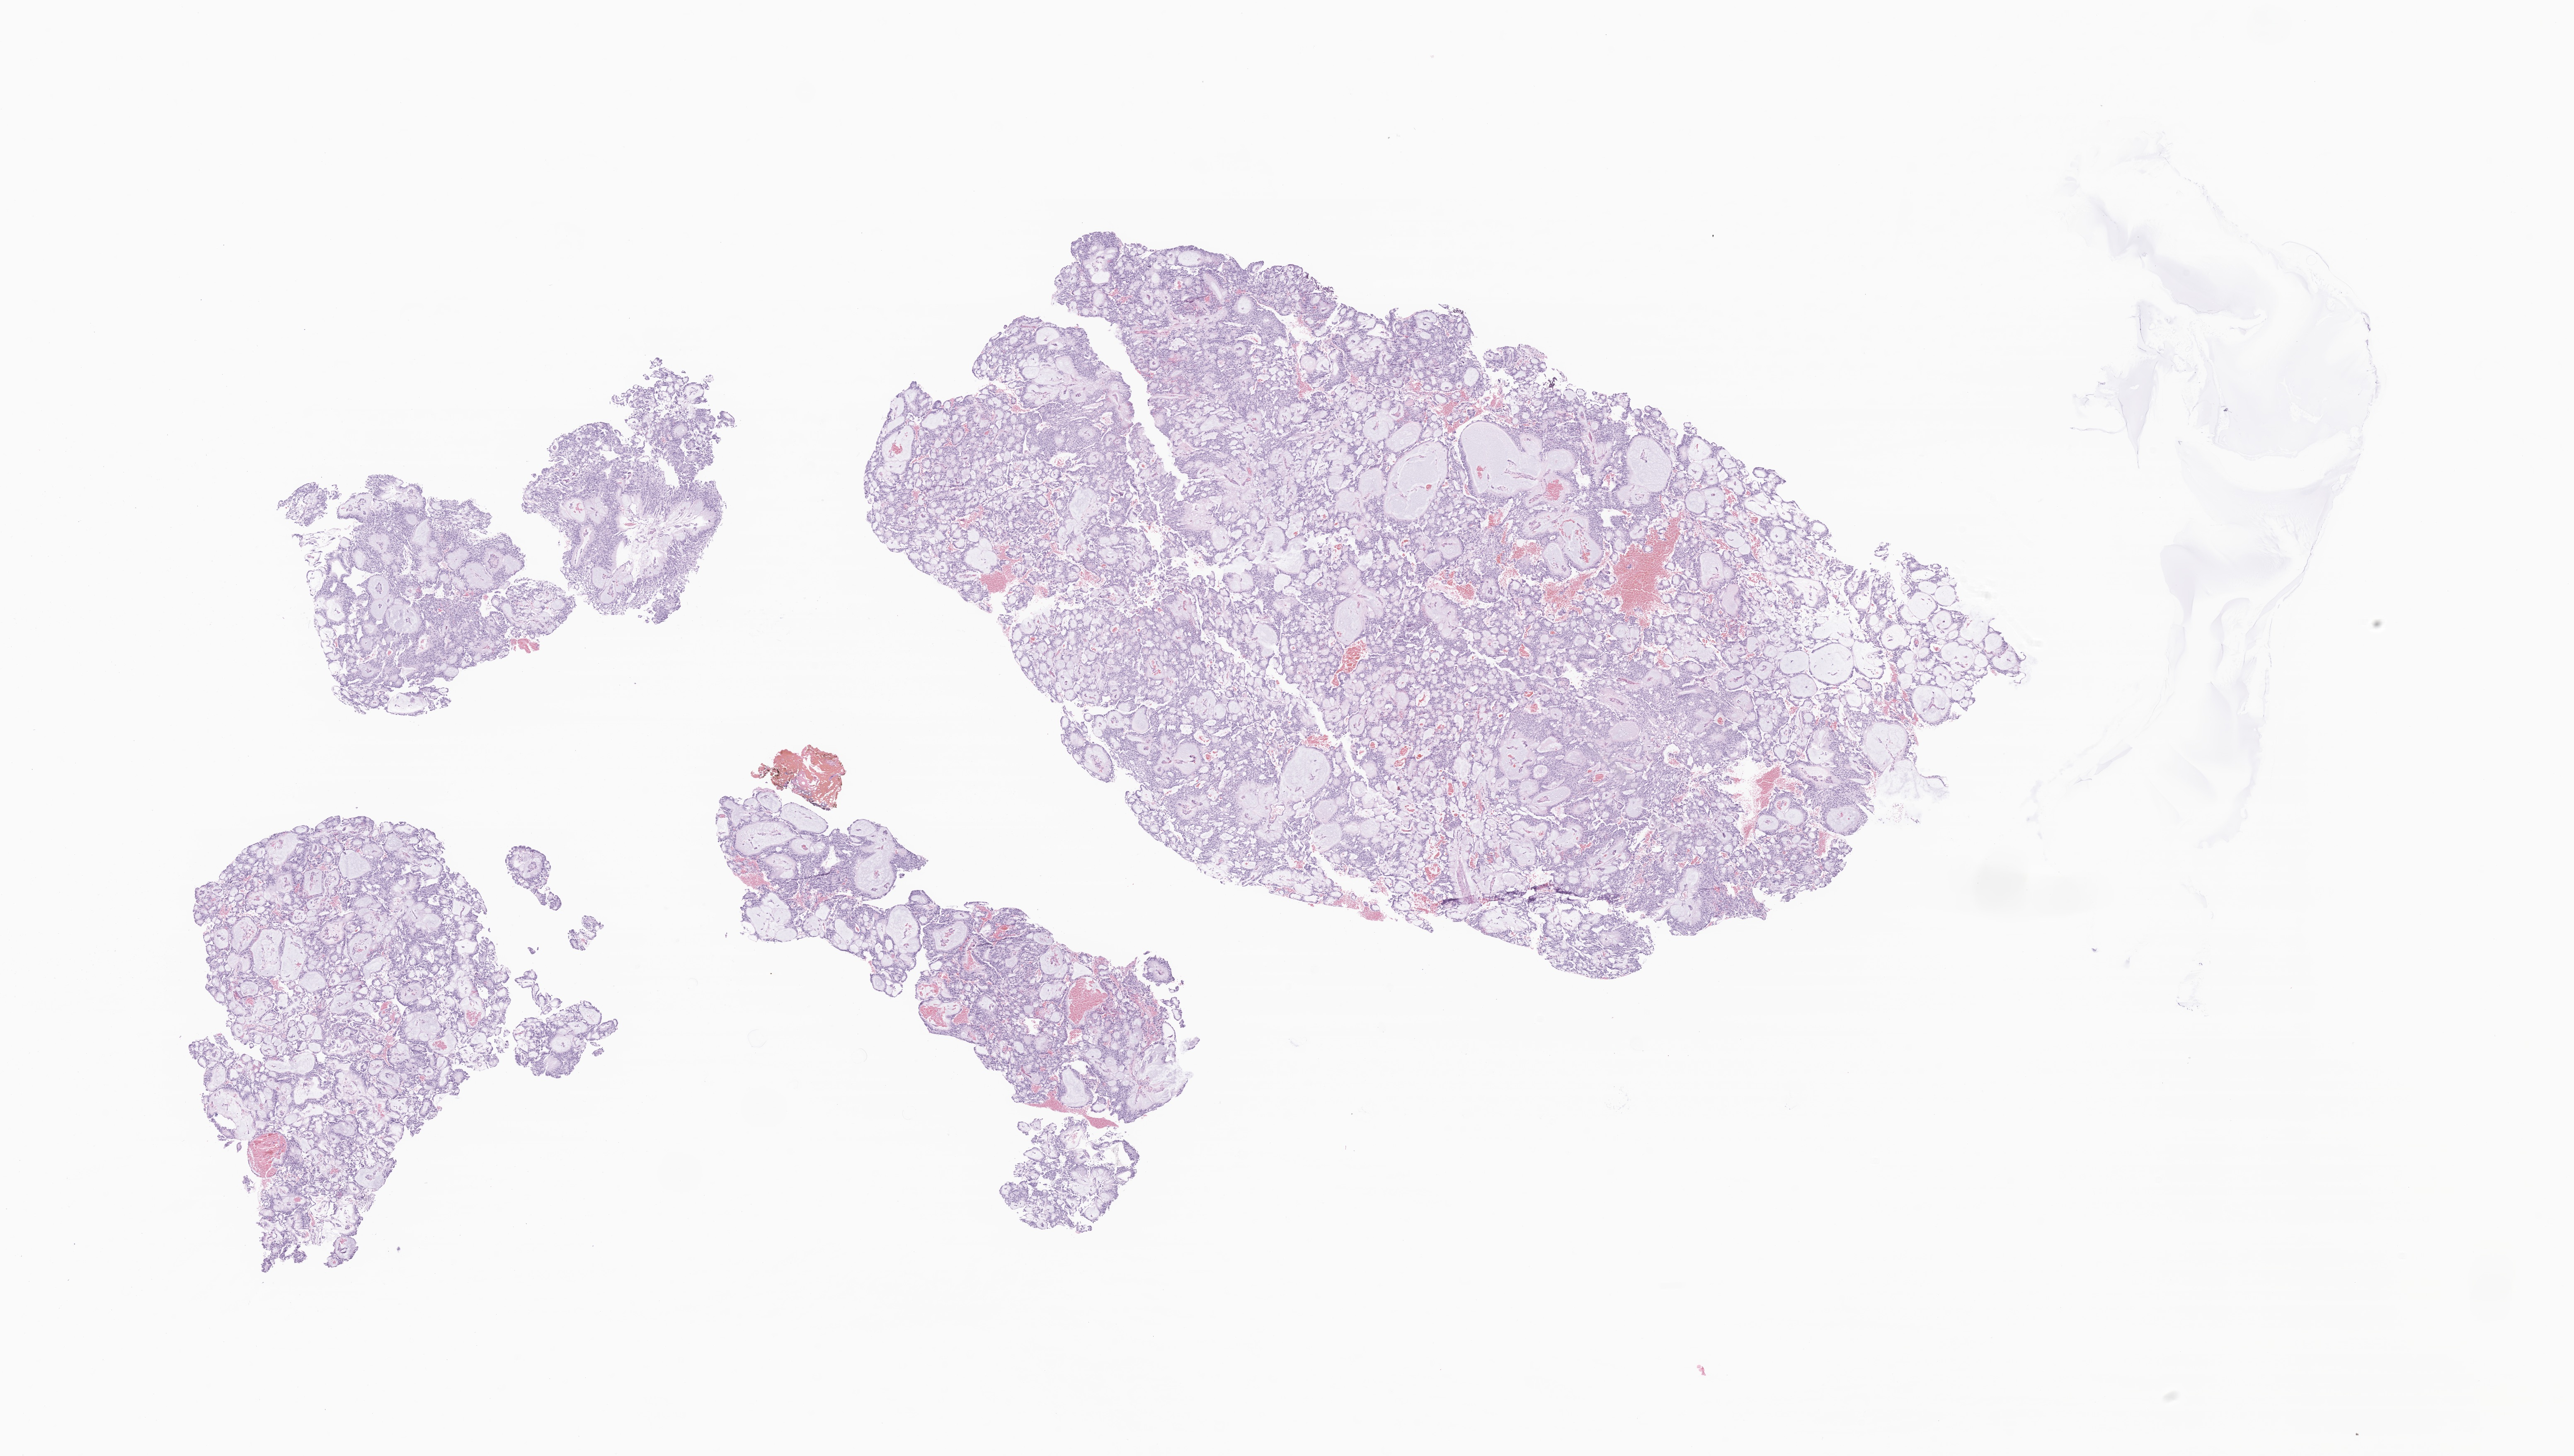
H&E whole-slide image of tumor tissue from the spinal cord — shown as a low-resolution overview of the whole scanned area (about 26.2 x 14.8 mm). Formalin-fixed paraffin-embedded section. Male patient, age 255 months.
Recorded diagnosis: Myxopapillary ependymoma.